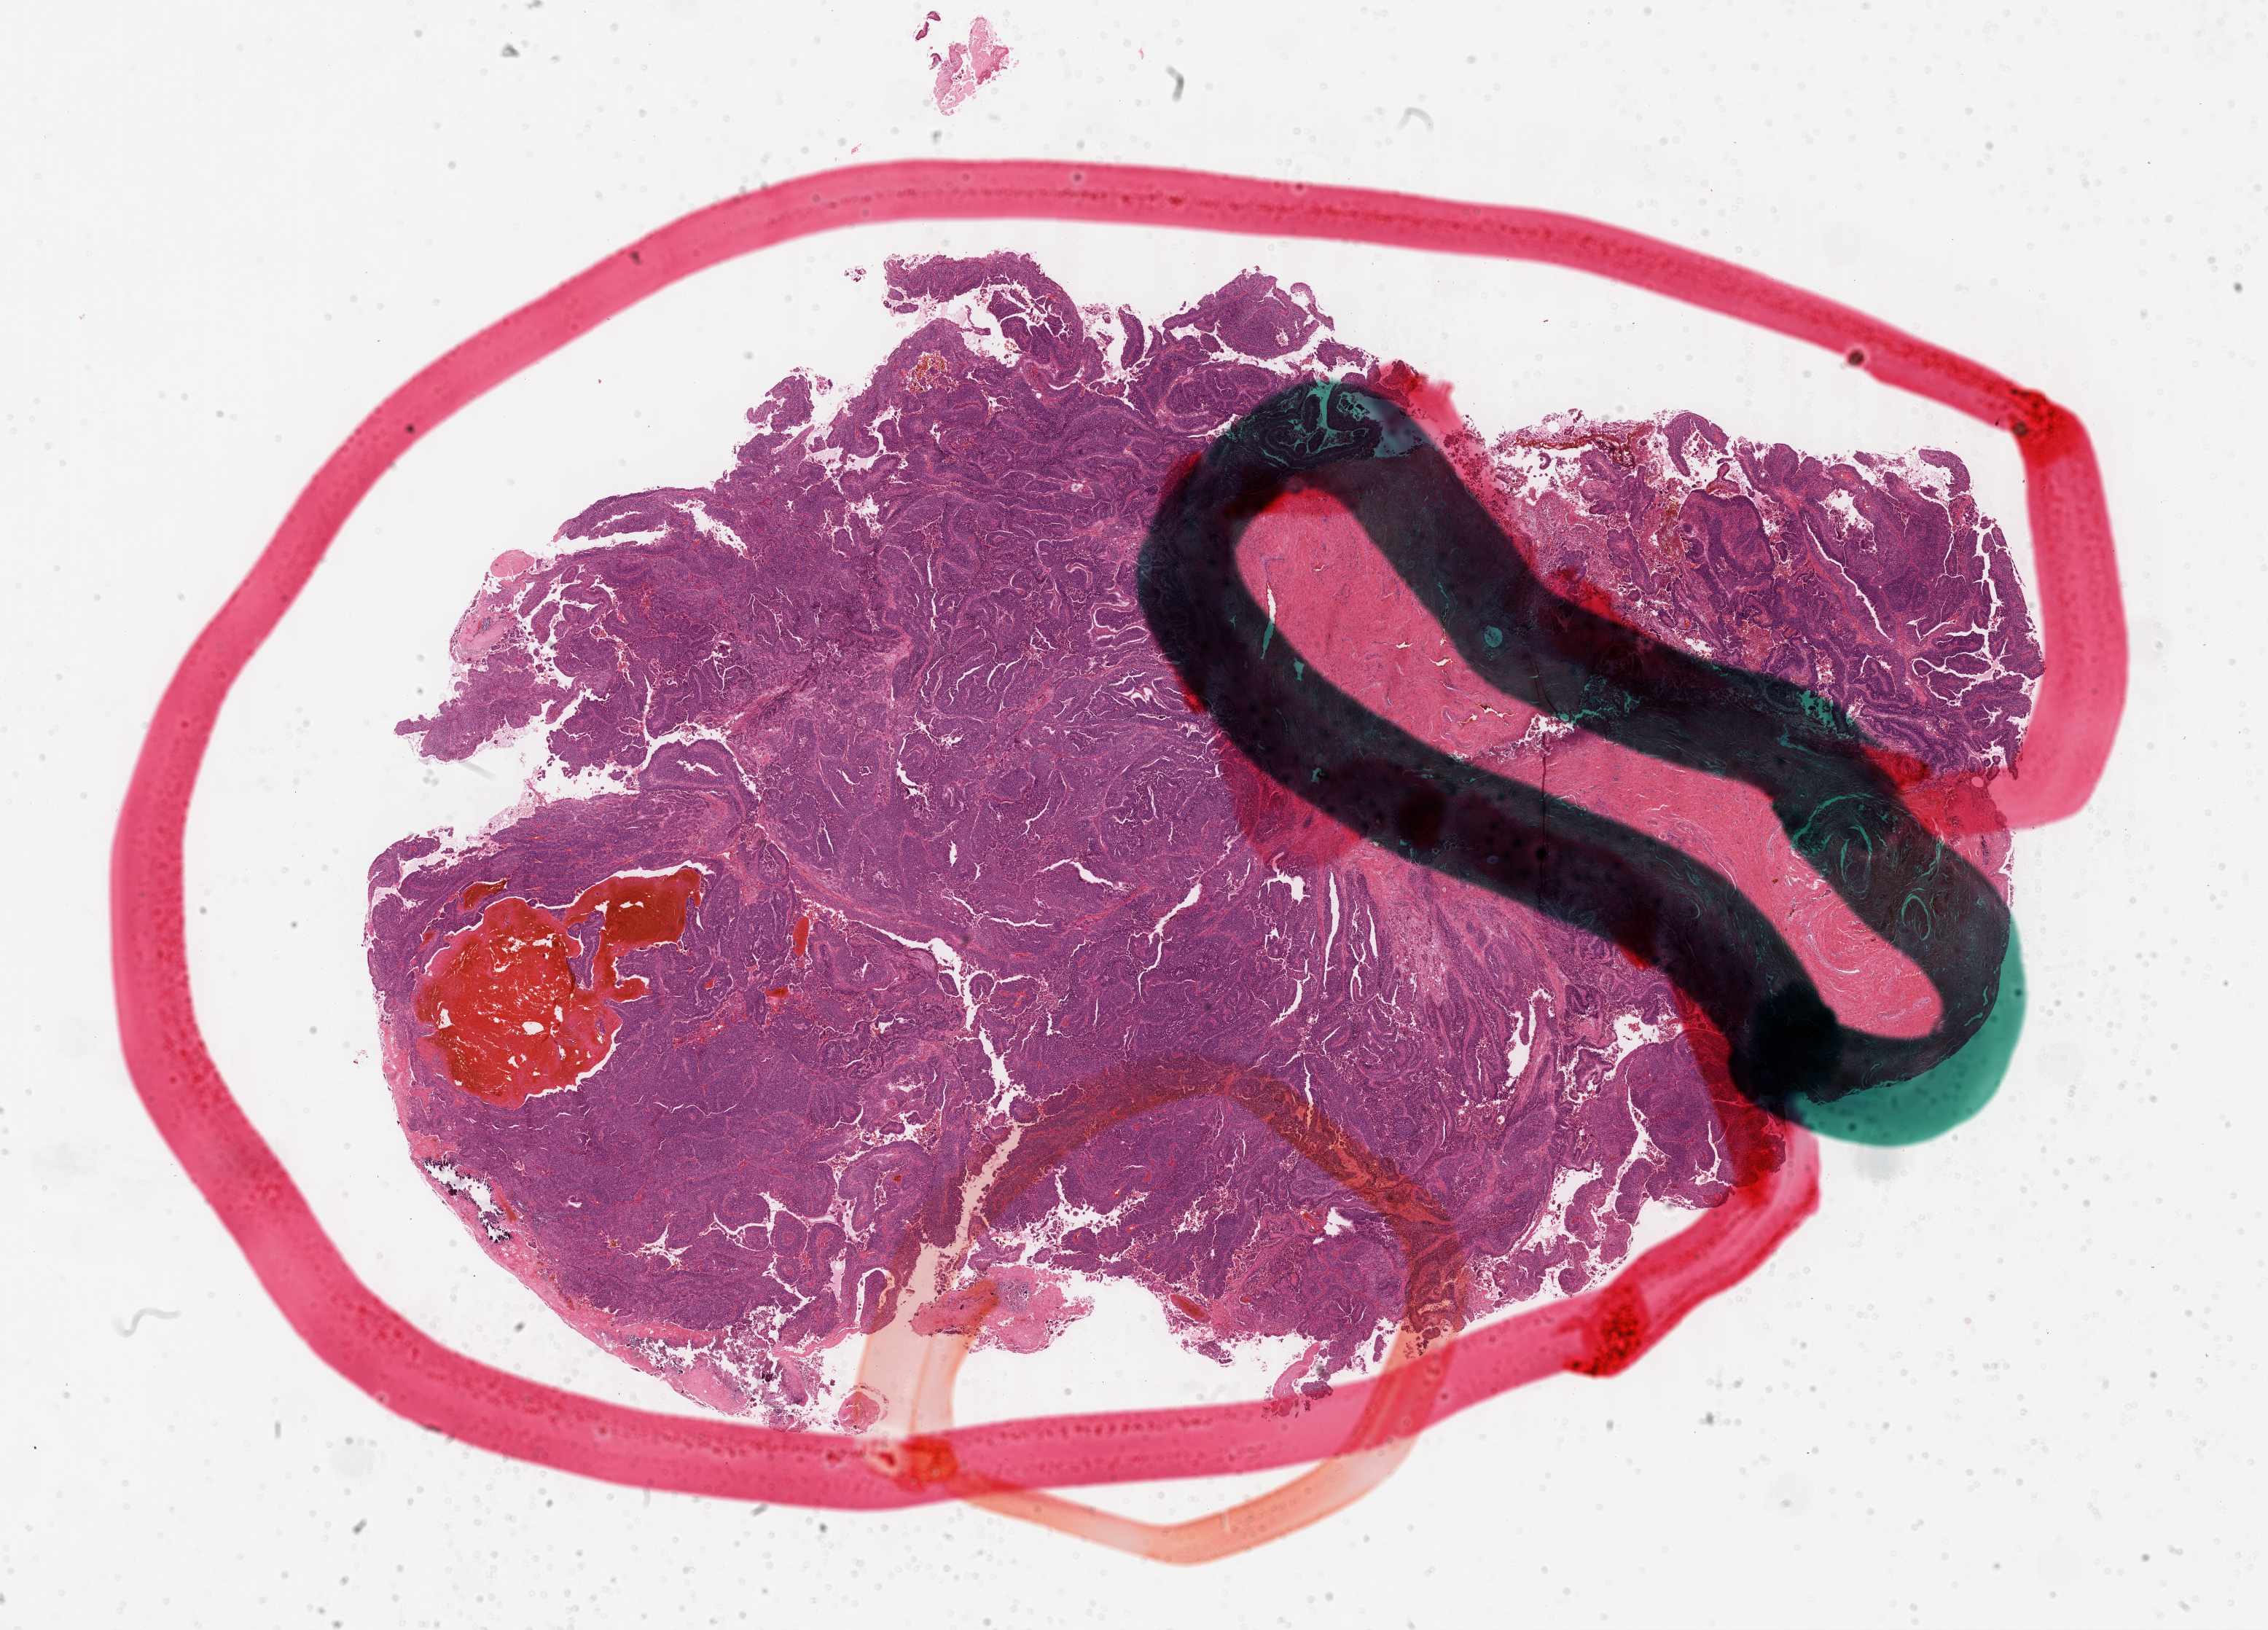
H&E-stained whole-slide image, a low-resolution overview of the entire scanned area, about 25.2 x 18.1 mm, formalin-fixed paraffin-embedded (FFPE) diagnostic section, primary tumour sample from the bladder. Male, age 59 years at initial diagnosis. Histologic grade: high grade.
Diagnosis: Transitional cell carcinoma. TNM: T2 N0 M0. AJCC pathologic stage: II.